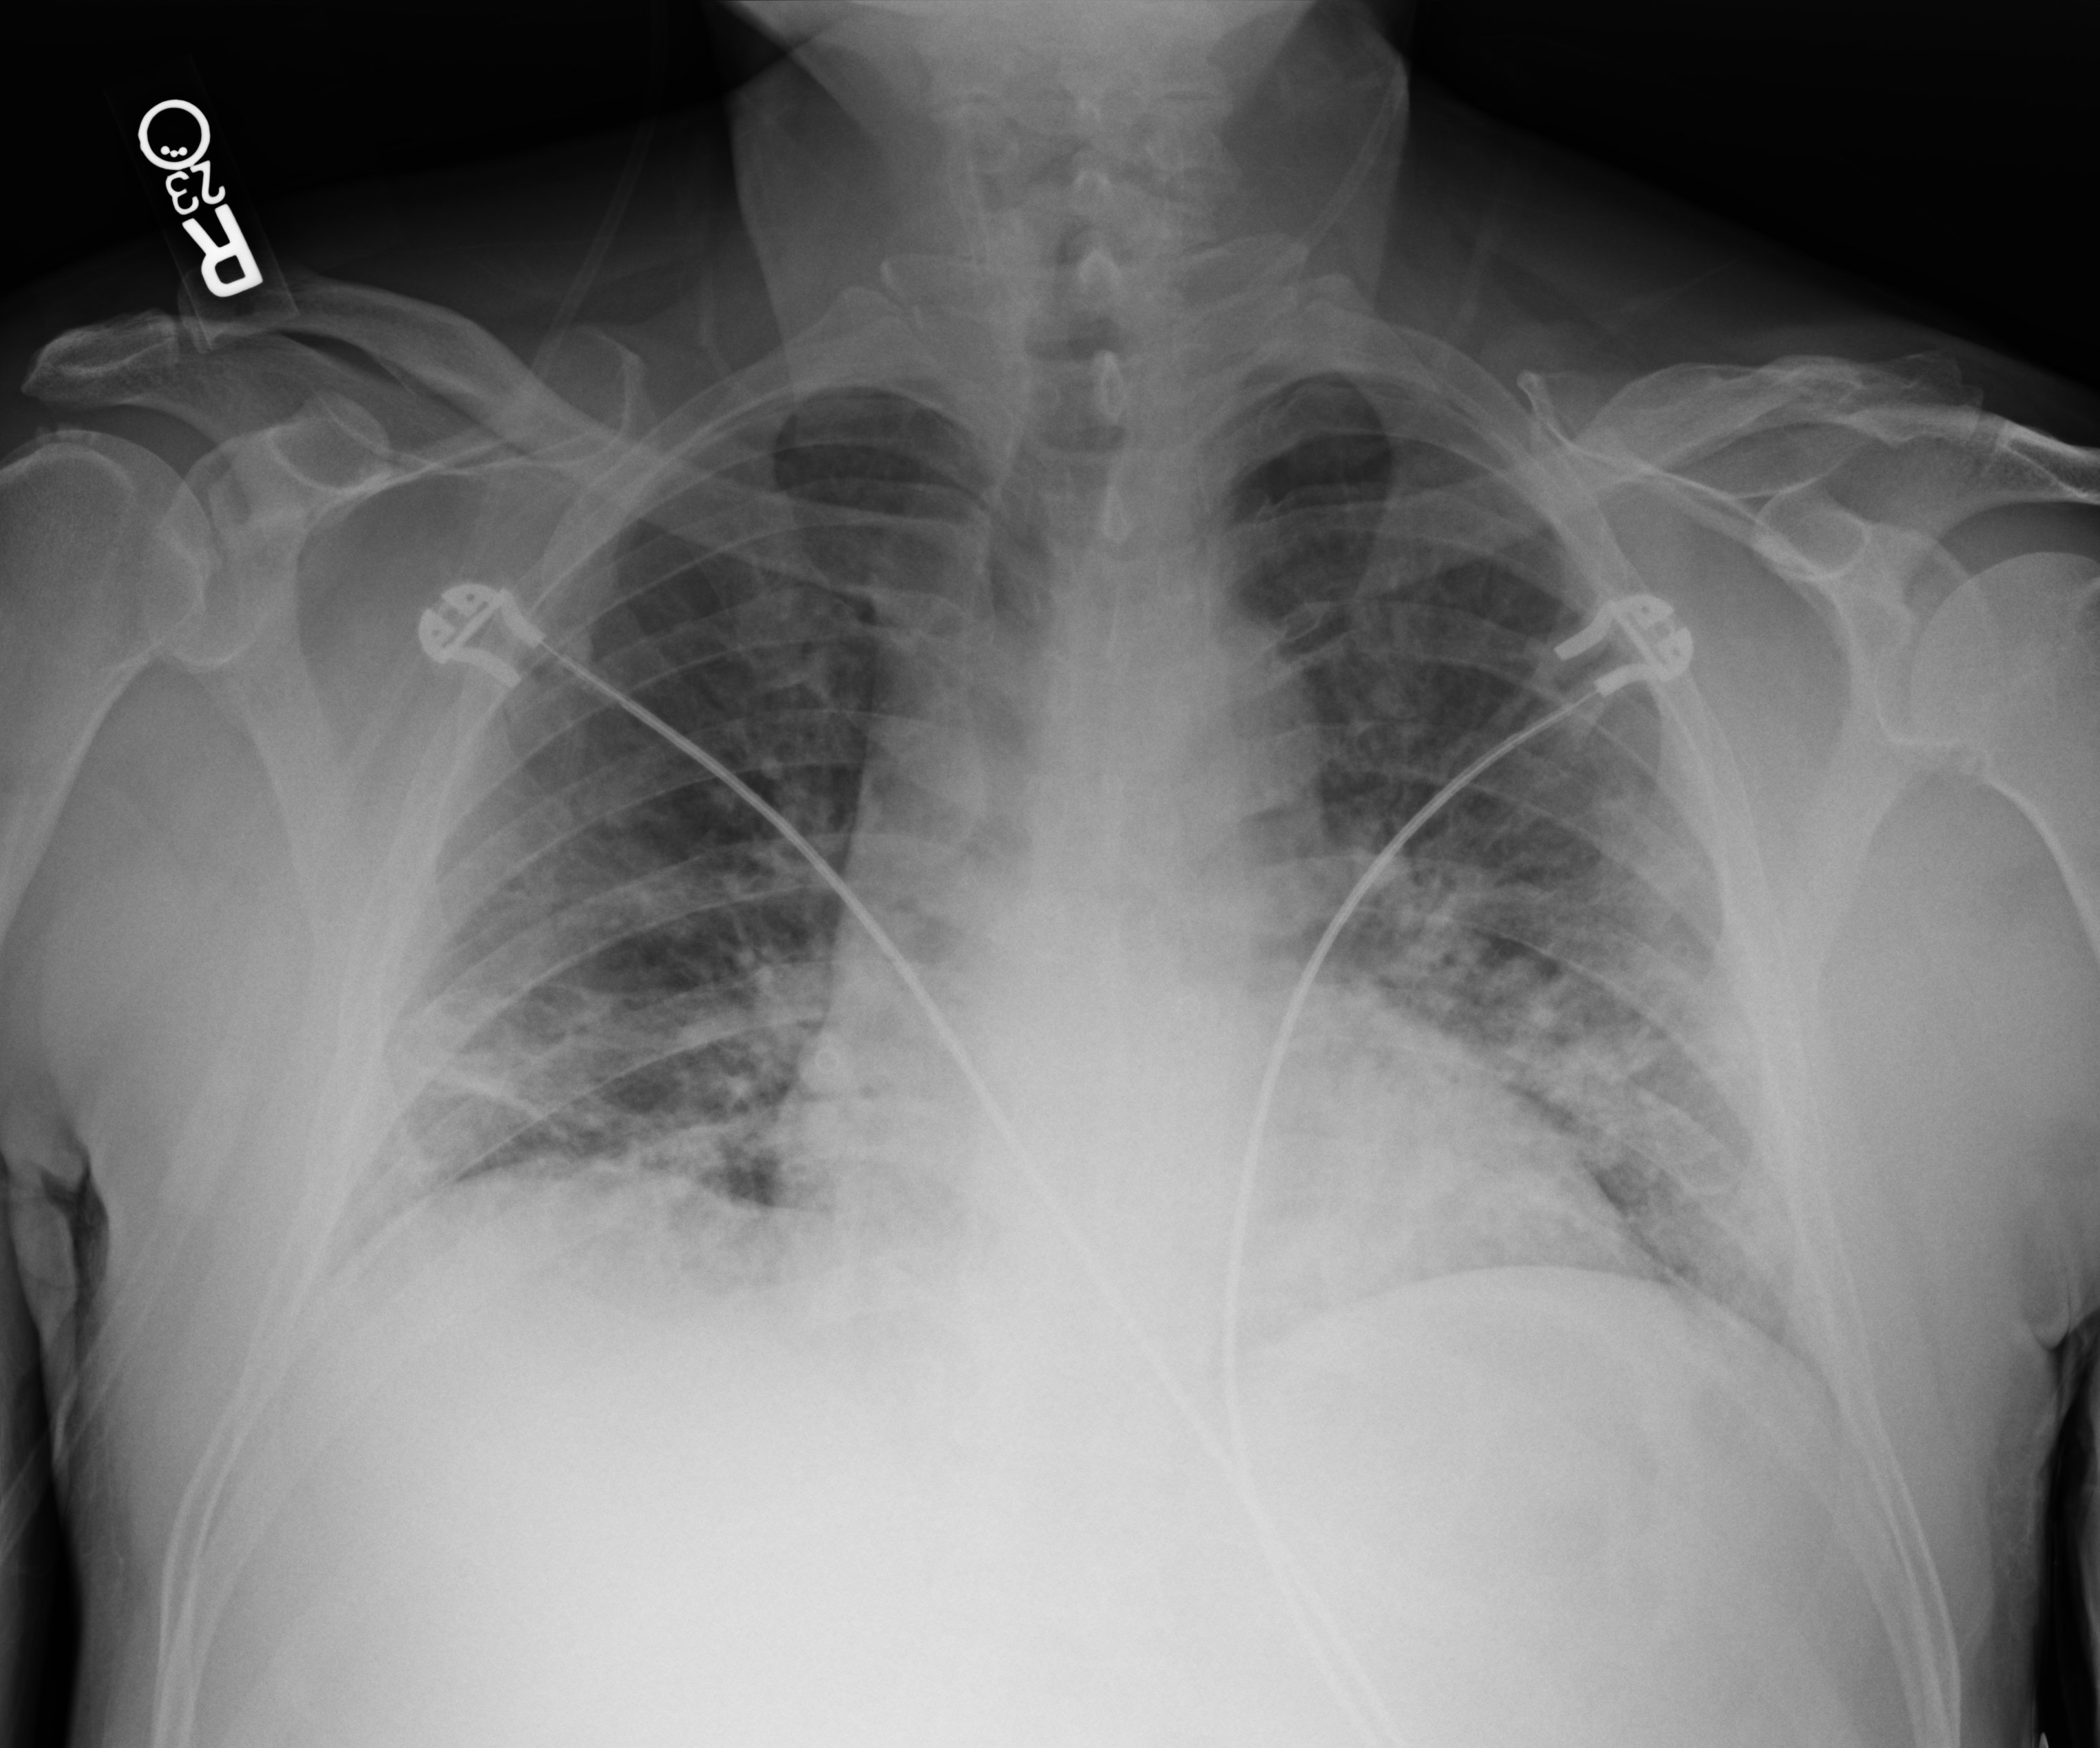
Bedside chest radiograph (computed radiography); anteroposterior (AP) projection. Patient hospitalised with COVID-19; male, aged 18–59 years.
From the hospital-stay record, not from the radiograph (when in the stay this image was taken is not recorded): admitted to intensive care during this hospital stay: no; diabetes (admission record): yes.